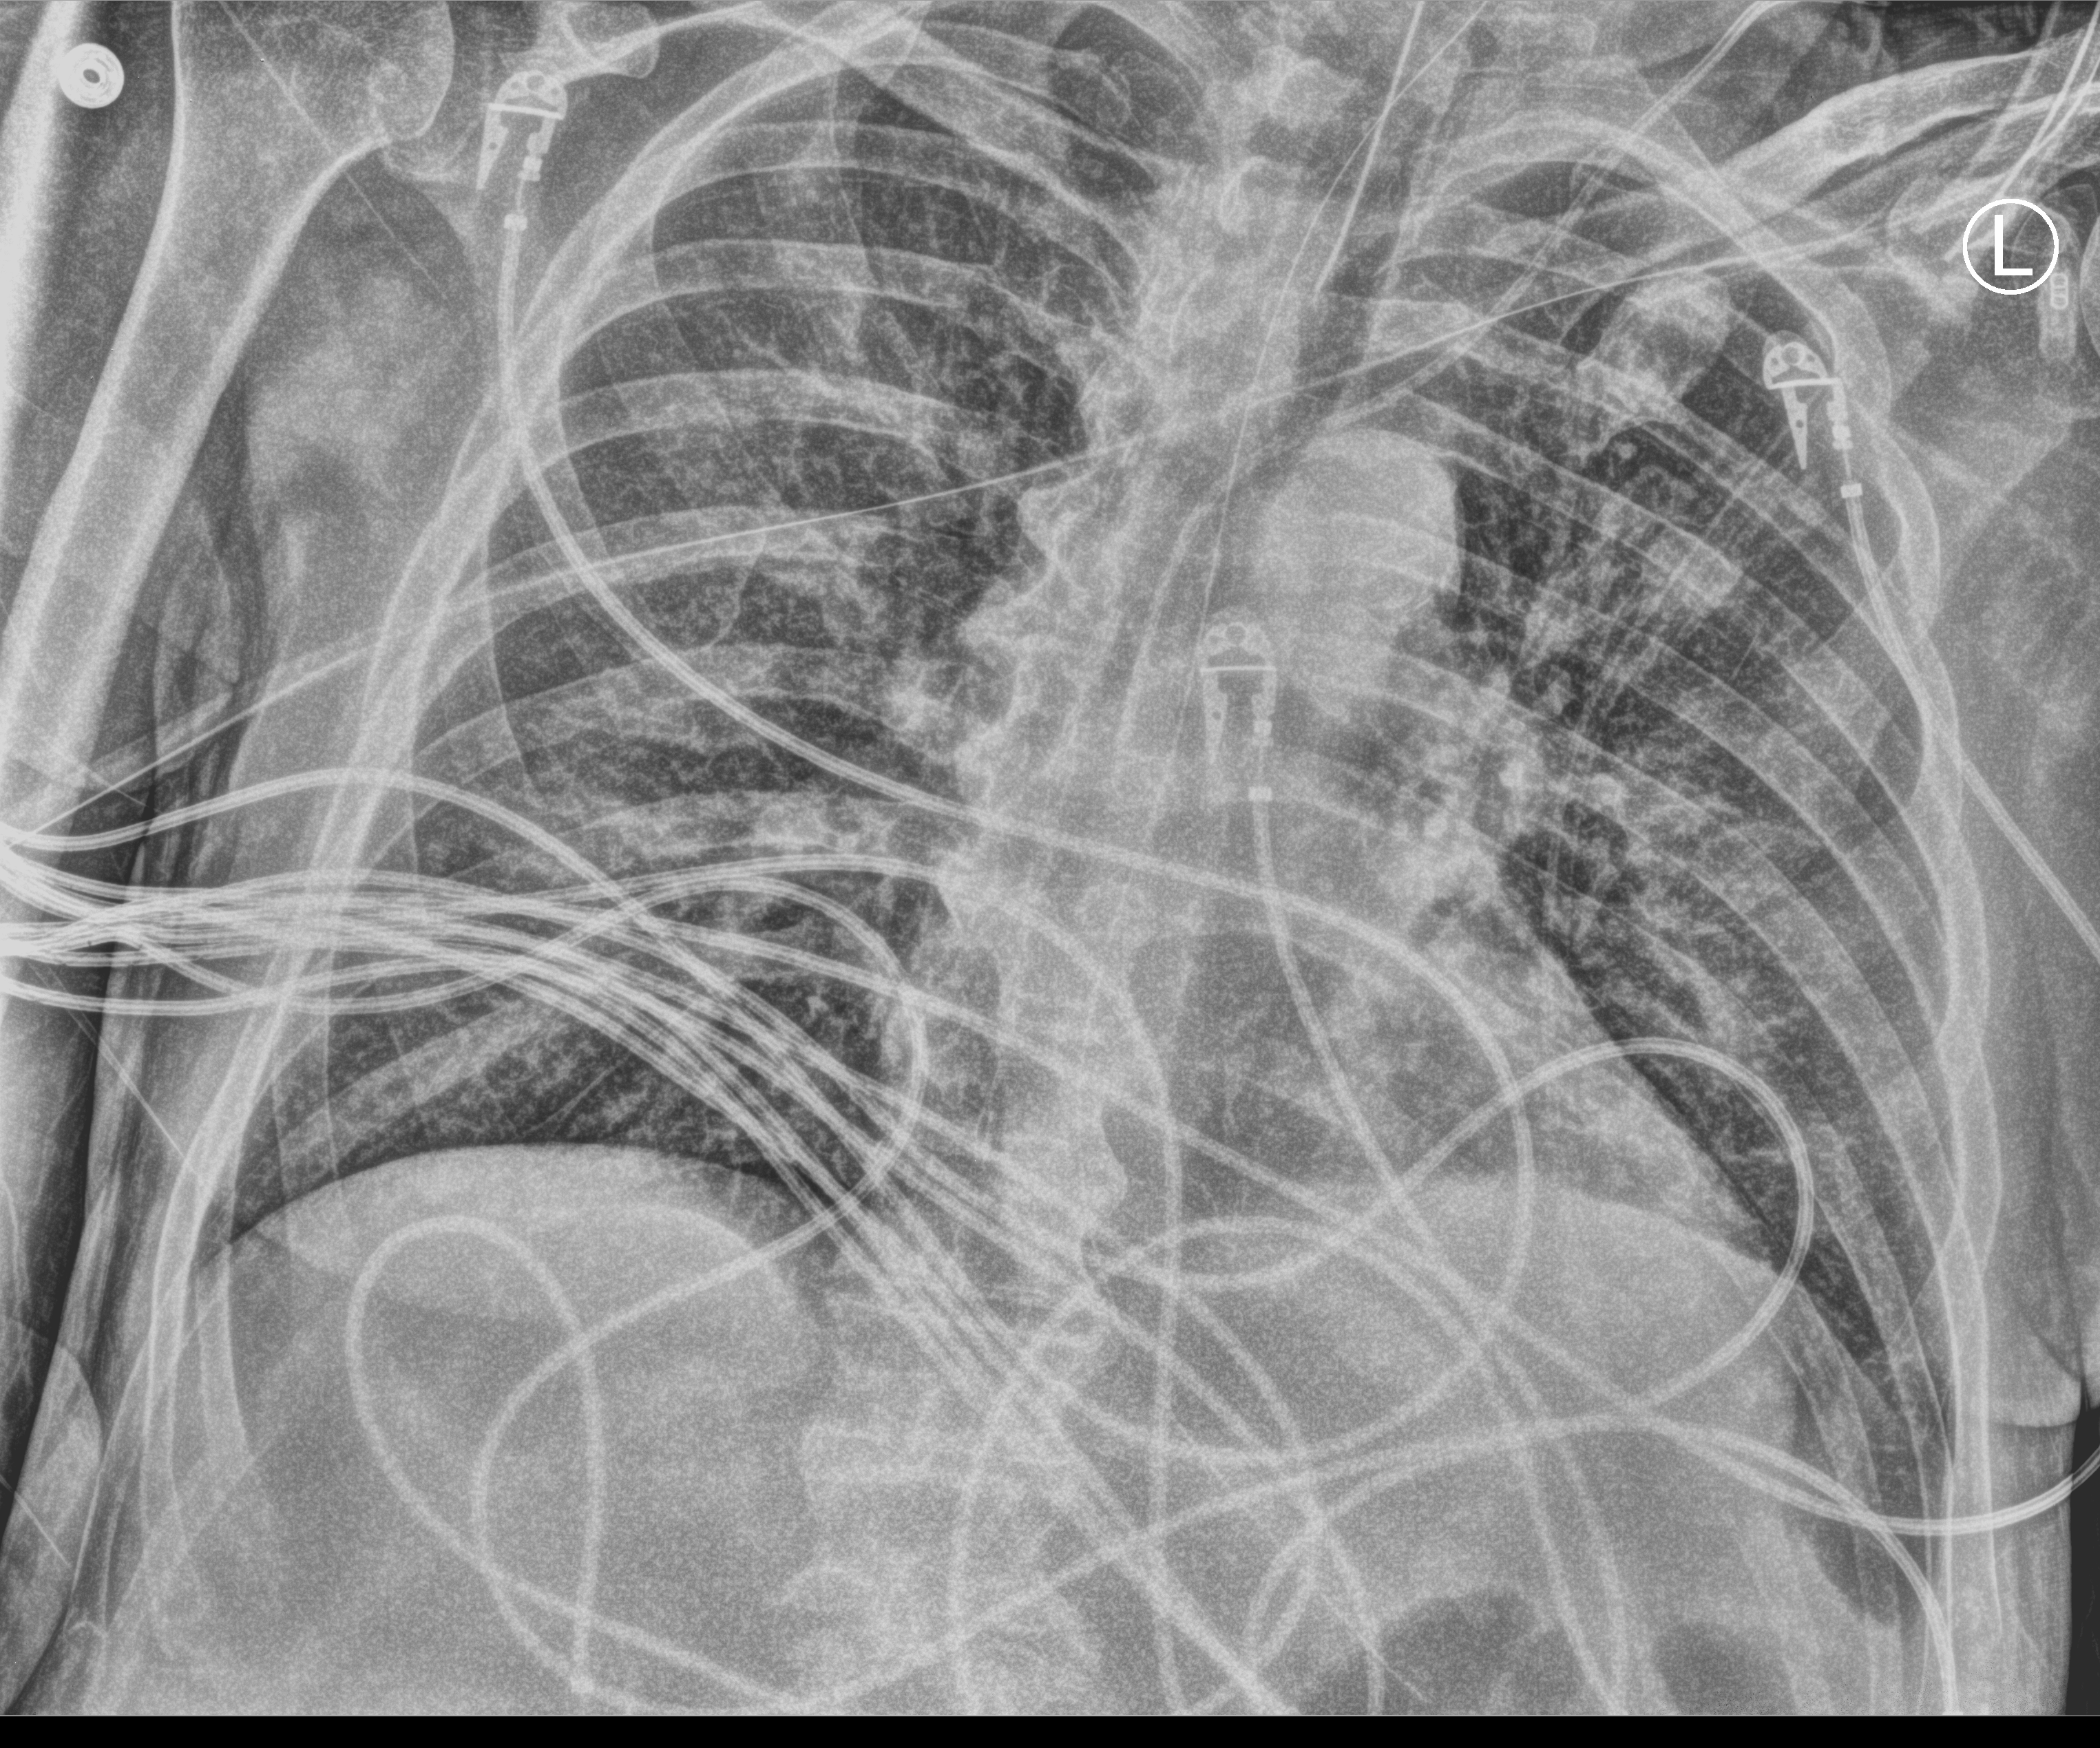
Portable chest radiograph; anteroposterior (AP) projection. Patient hospitalised with COVID-19; male, aged 60–74 years.
Admission-level facts for this patient (not findings on this image; timing relative to this image not recorded):
- length of hospital stay: 22 days